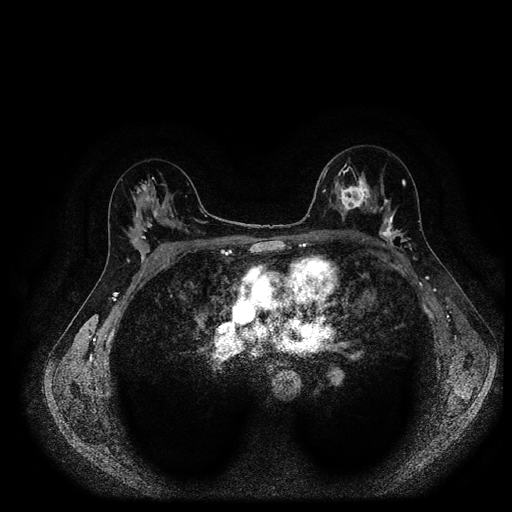
Breast MRI (dynamic contrast-enhanced, multi-phase), one axial slice. Slice 61 of 116 in the series (ordered by position). Dynamic contrast-enhanced series, time point 2 of 5 at this slice position (early post-contrast). 1.5 T. TE 2.7 ms, TR 5.4 ms. 2 mm slice thickness. 512 × 512 image matrix, field of view 340 × 340 mm. Patient: female, 40 years.
Structures marked on this image (semi-automatic segmentation, software-assisted and operator-edited):
- breast lesion (labelled 'tumour' in the annotation; benign lesions carry a separate 'benign' label): bounding box [x1, y1, x2, y2] px = [334, 174, 371, 215]